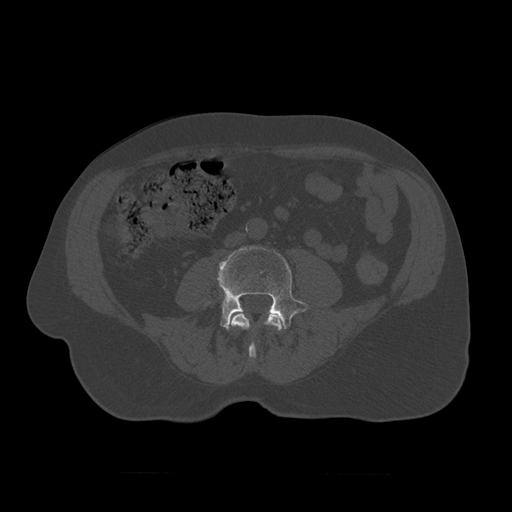
CT including the spine, one axial slice. Reconstruction kernel STANDARD. Bone window (W 1800 / L 400 HU). 1.25 mm slice thickness. 512 × 512 image matrix, field of view 405 × 405 mm. Patient age 75 years. From the clinical record (not read from this slice): primary cancer: prostate.
Annotated regions visible in this slice (semi-automatic segmentation, software-assisted and operator-edited):
- L3 vertebra: box from (x=229, y=310) to (x=284, y=359) px
- L4 vertebra: (x=217, y=246)–(x=309, y=330)